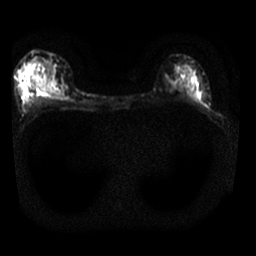
Breast MRI, one axial slice; slice 16 of 25 in the series (ordered by position); diffusion-weighted series; image 2 of 4 stored at this slice position (different b-values; order by instance number); 1.5 T; 4 mm slice thickness; 256 × 256 image matrix, field of view 310 × 310 mm. Female patient.
Outlined on this slice (manually delineated by an expert):
- tumour on diffusion-weighted imaging: bounding box <35,82,47,92> (left, top, right, bottom; pixels)